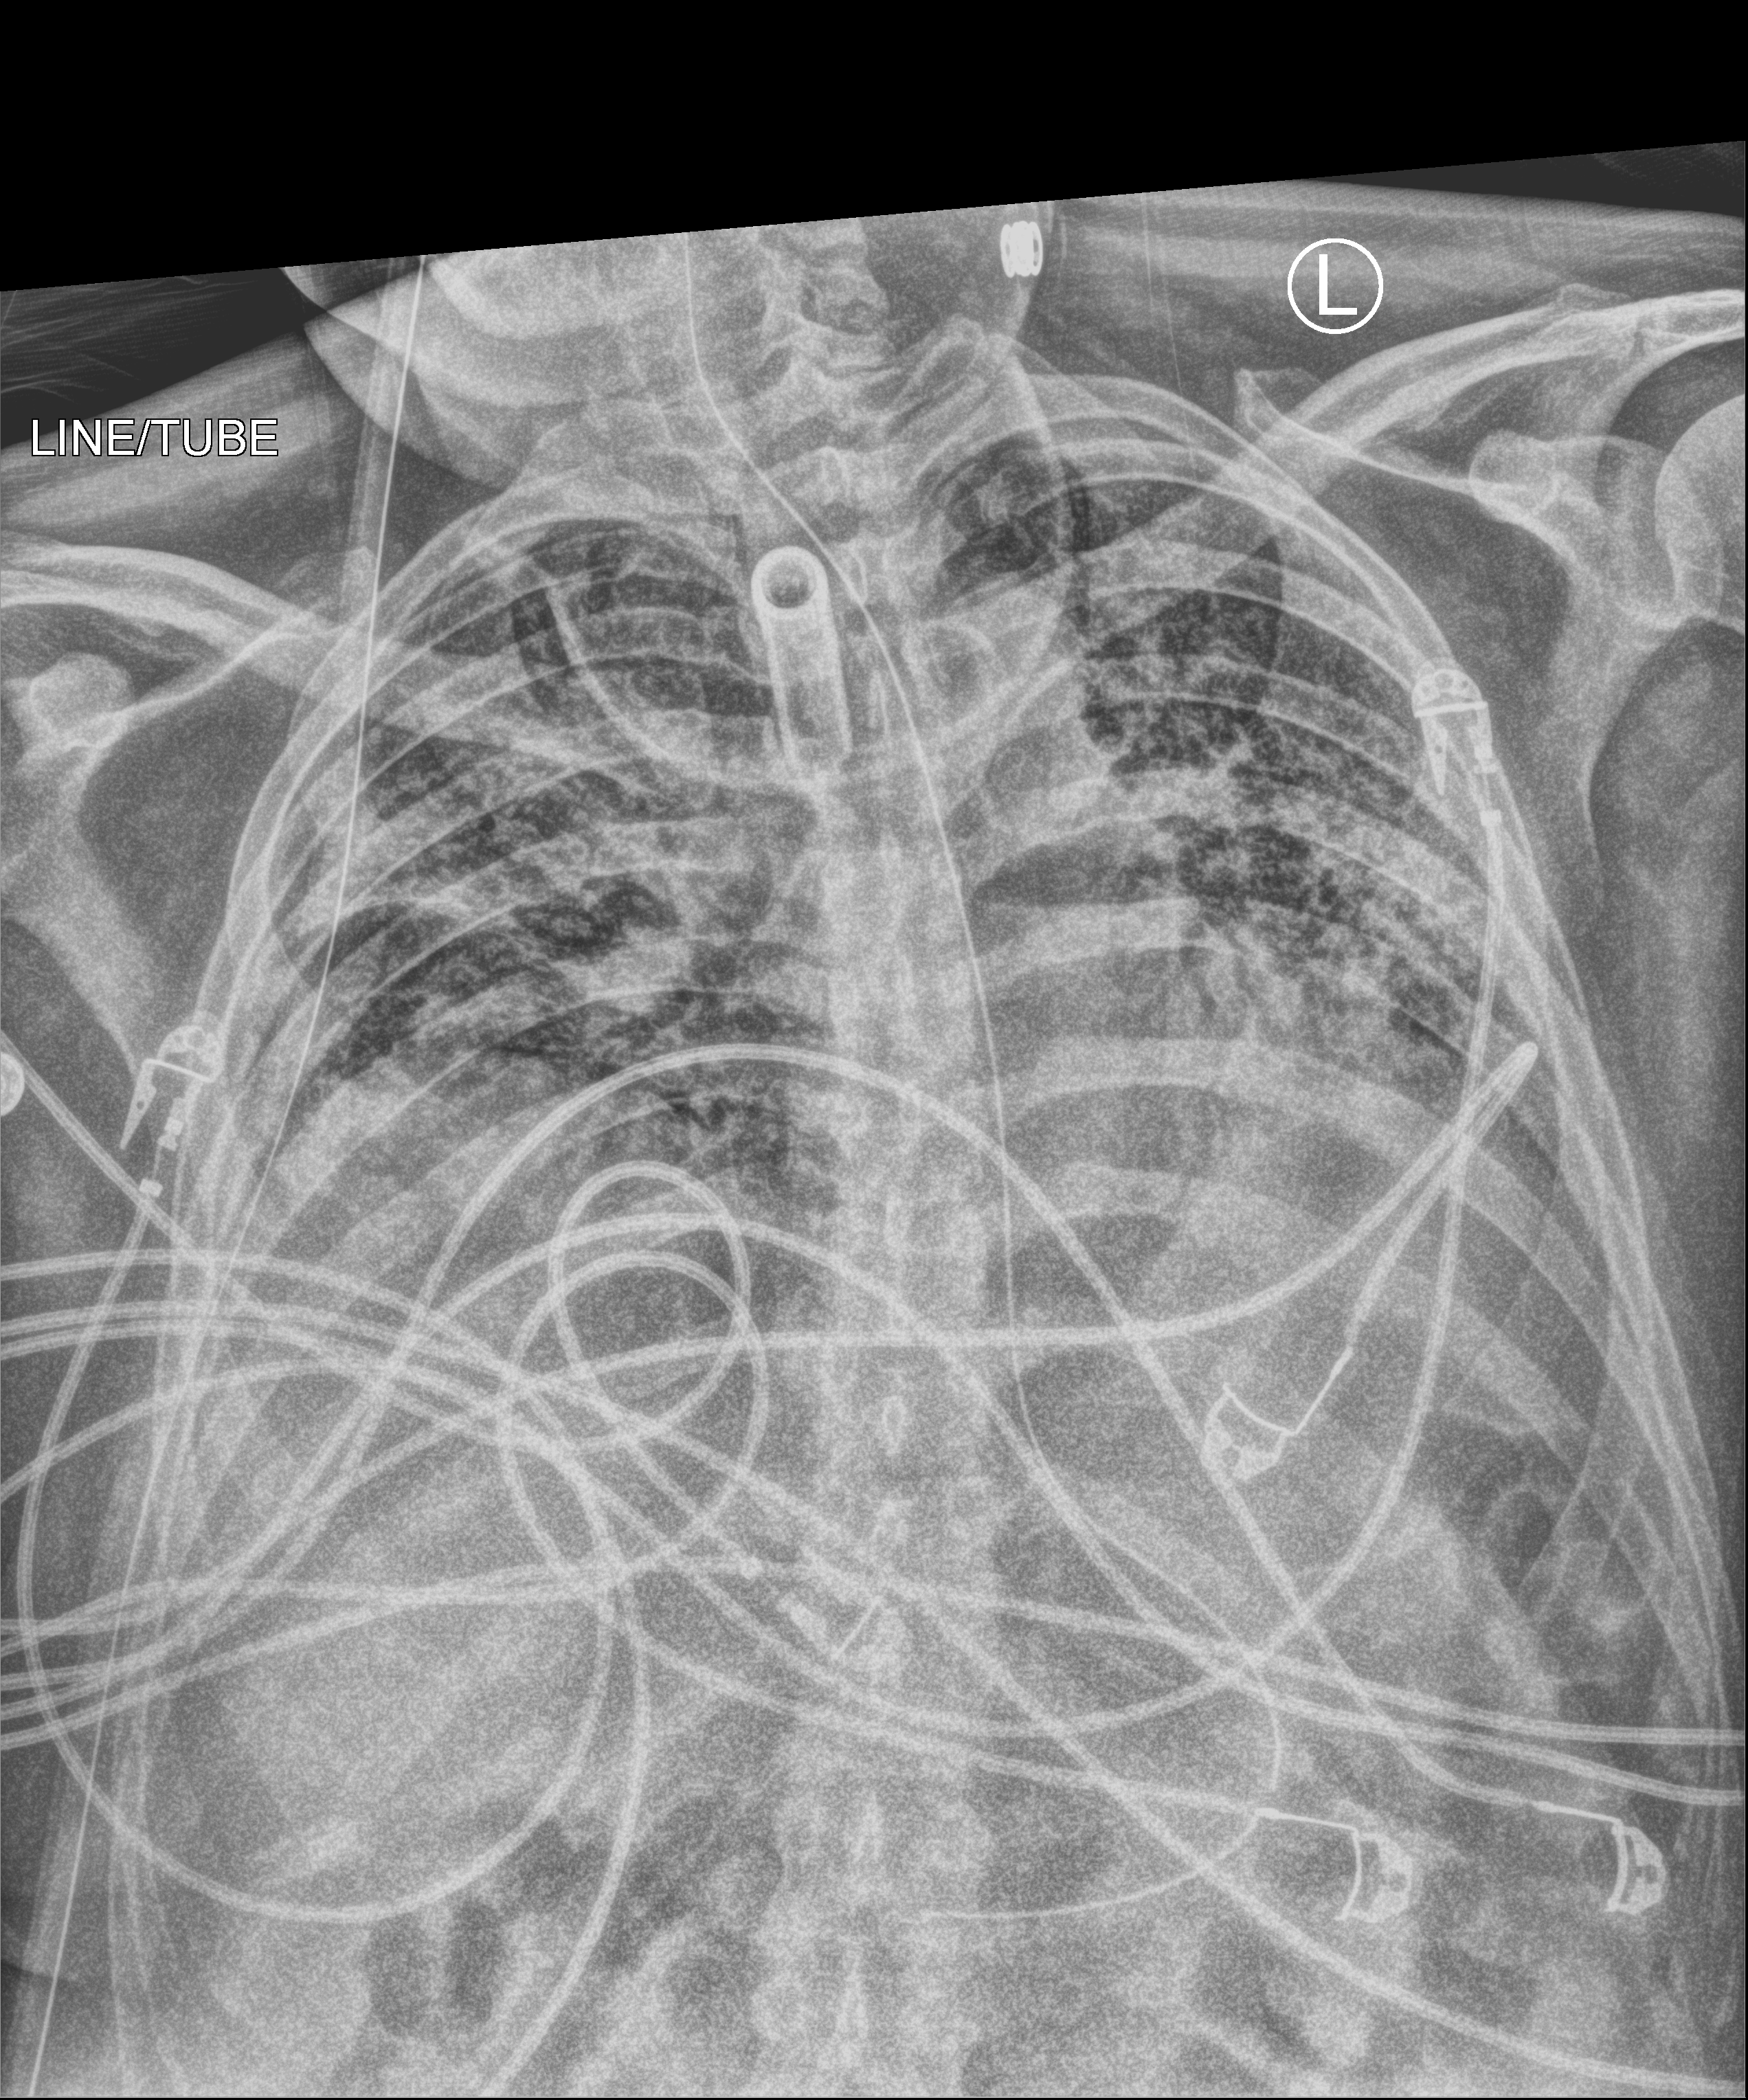
Bedside chest radiograph (computed radiography). Patient hospitalised with COVID-19; male, aged 18–59 years.
From the hospital-stay record, not from the radiograph (when in the stay this image was taken is not recorded):
- admitted to intensive care during this hospital stay: yes
- length of hospital stay: 96 days
- mechanically ventilated during this hospital stay: yes